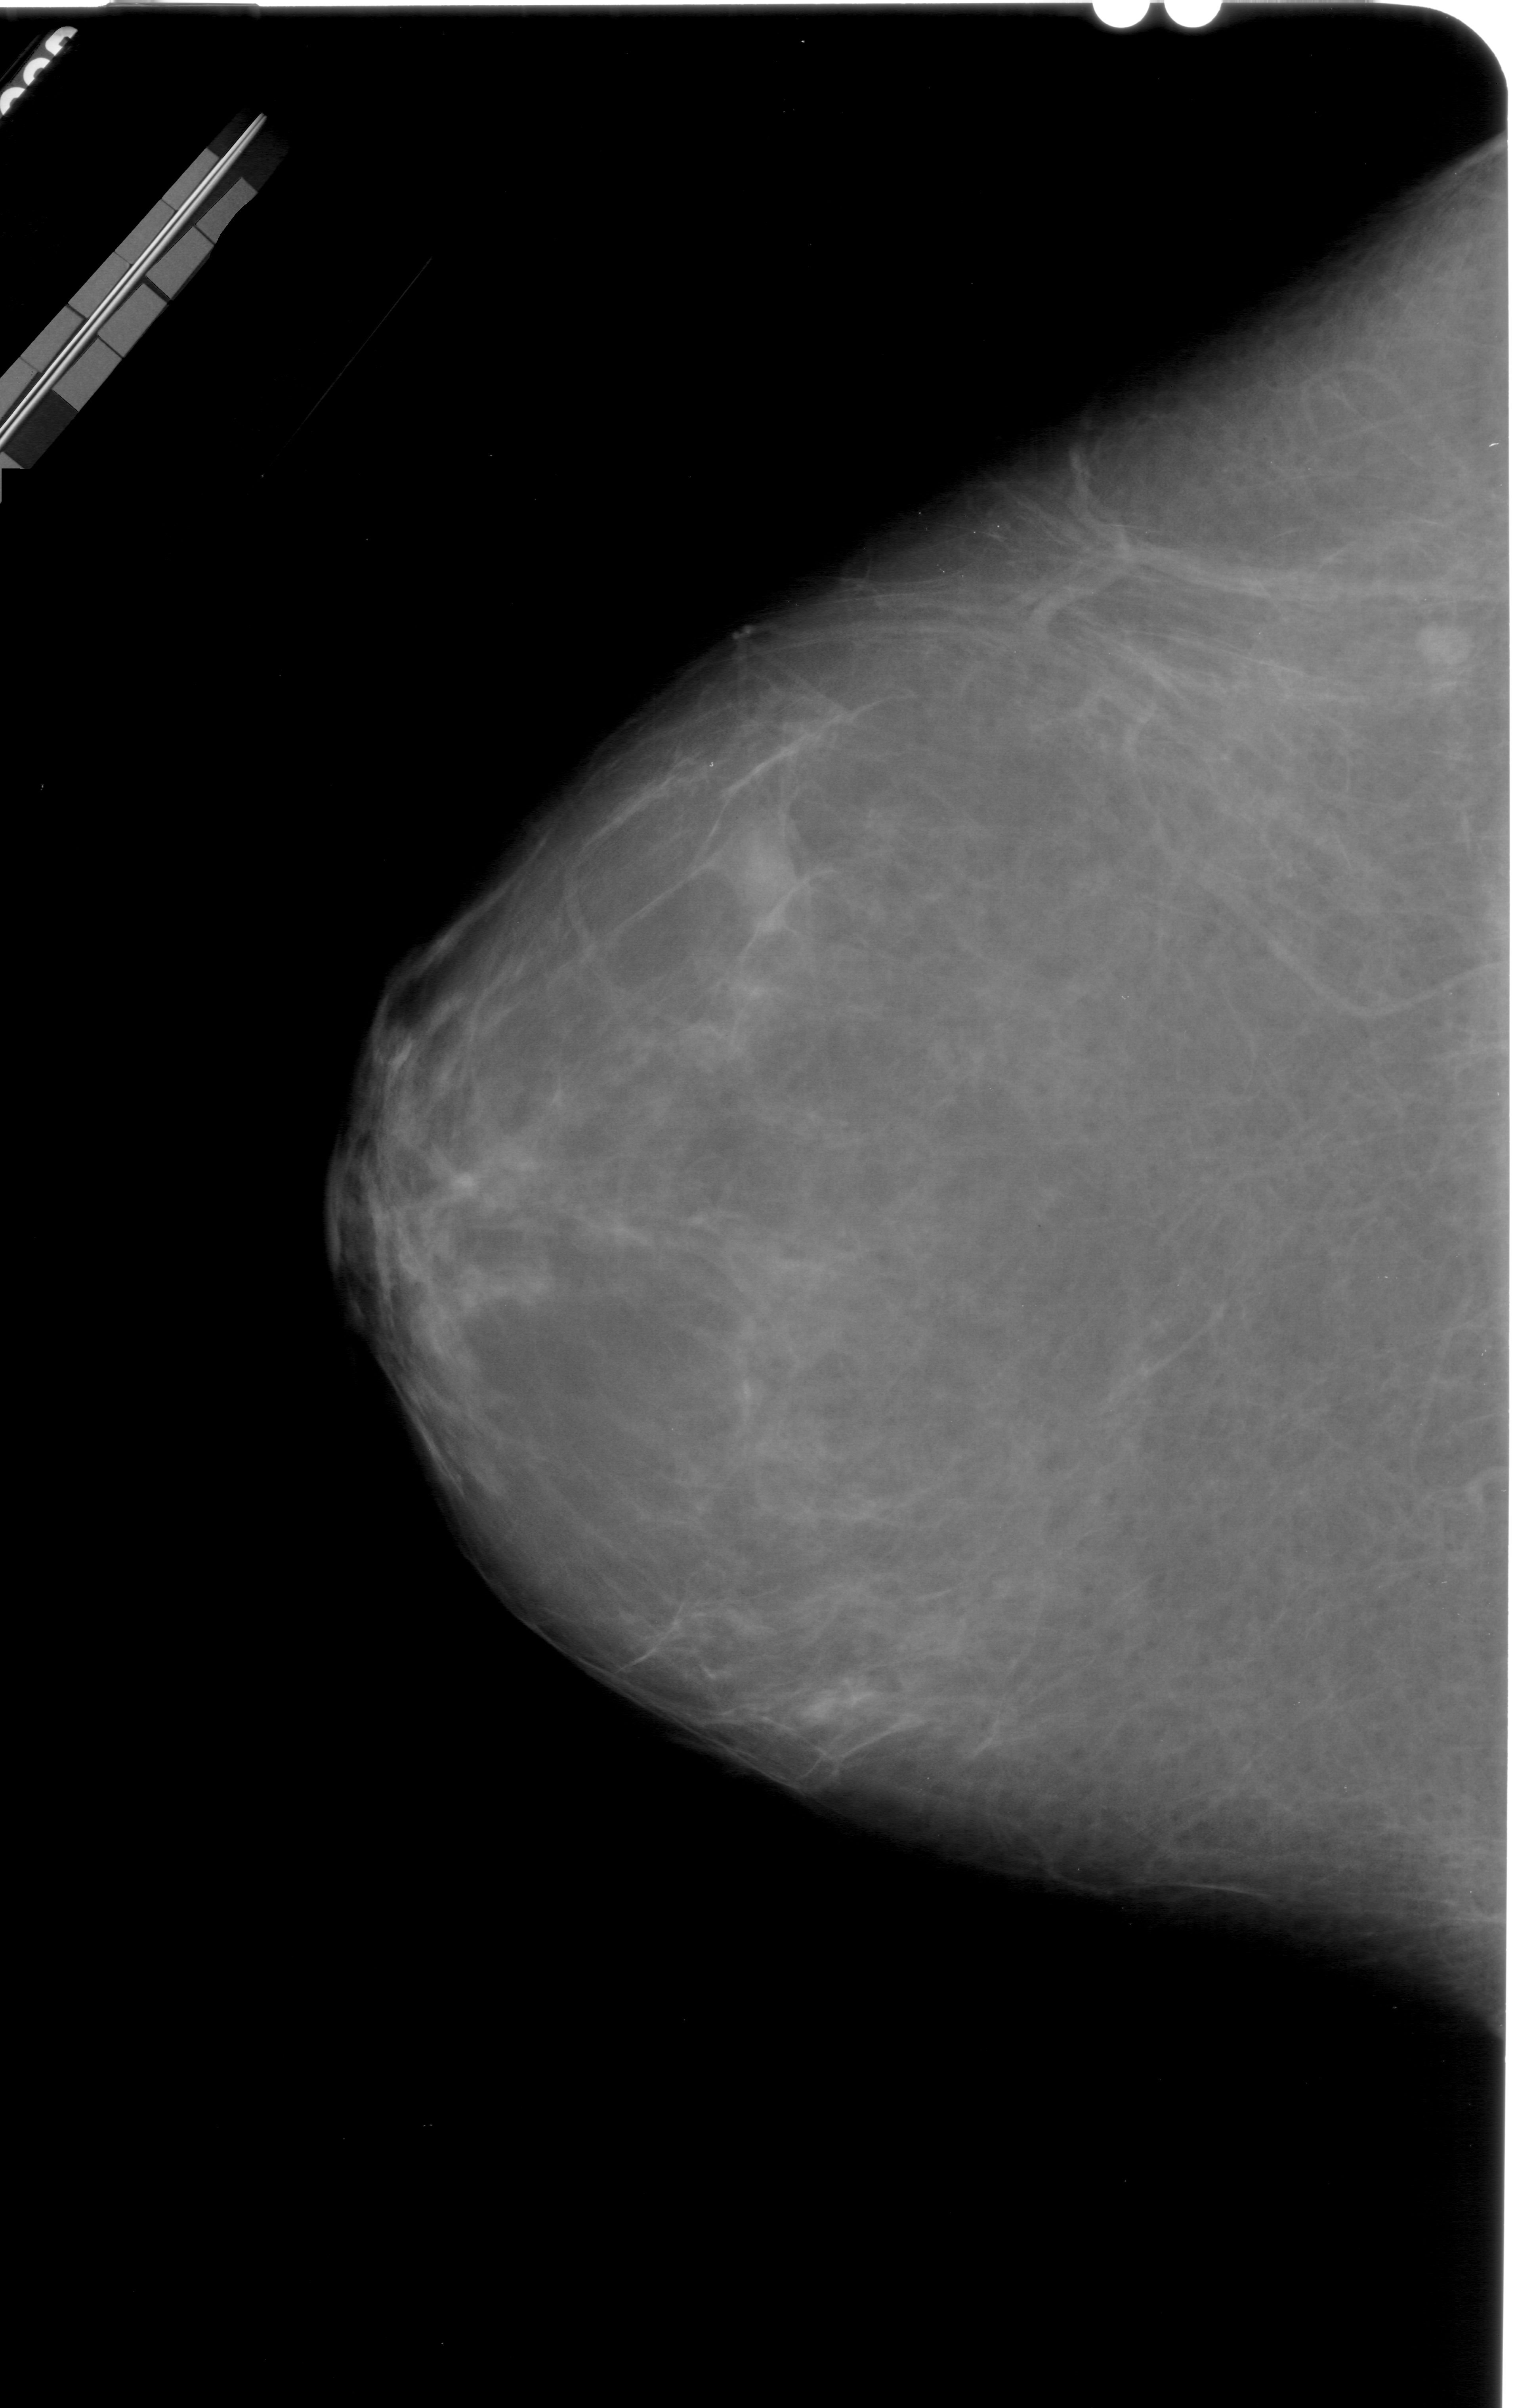
Digitized screen-film mammogram; left breast; craniocaudal (CC) view.
Radiologist-marked abnormalities on this image: mass, shape oval, margins ill defined; BI-RADS assessment category 4; pathology result (as recorded, not read from the image): benign.